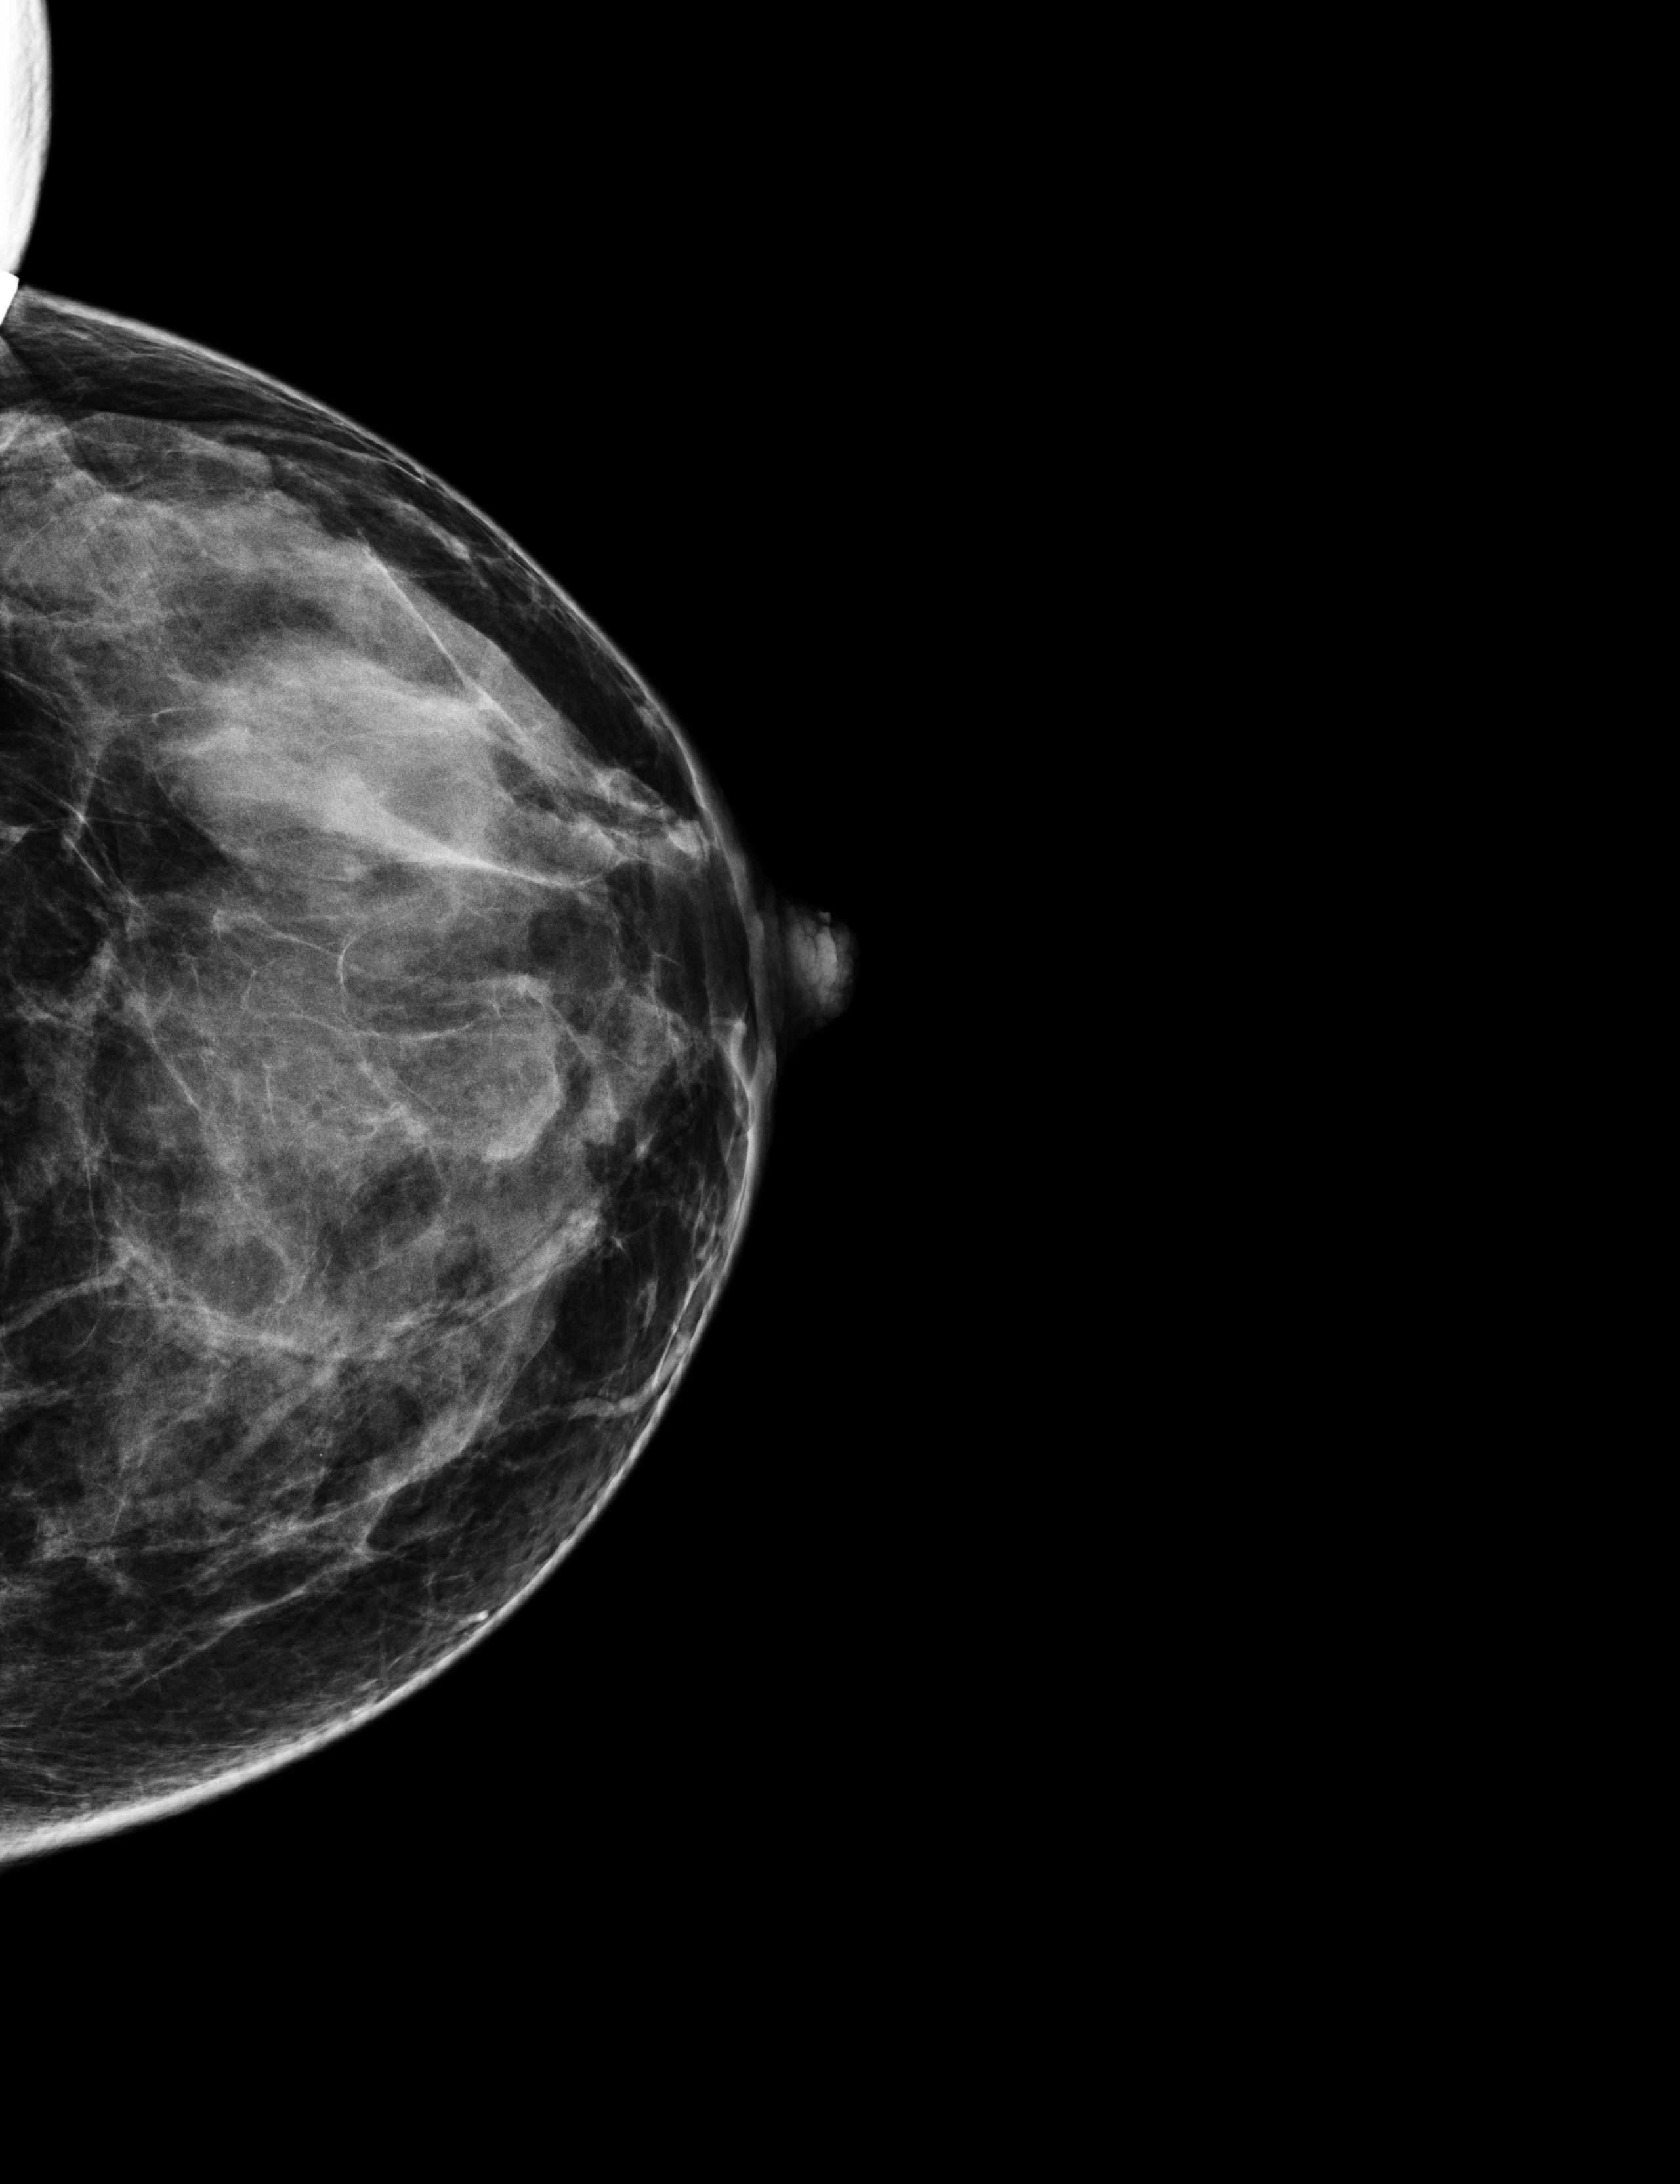
Full-field digital mammogram (FFDM), left breast, cranio-caudal projection, annual screening mammography examination, compressed breast thickness 44 mm, system: Selenia Dimensions. Female patient, age 49 years.
- BI-RADS breast density category at the screening exam (both breasts, scale 1–4): 3
- final BI-RADS category for the screening round (tomosynthesis exam, both breasts): category 1
- recall: no recall after this screen